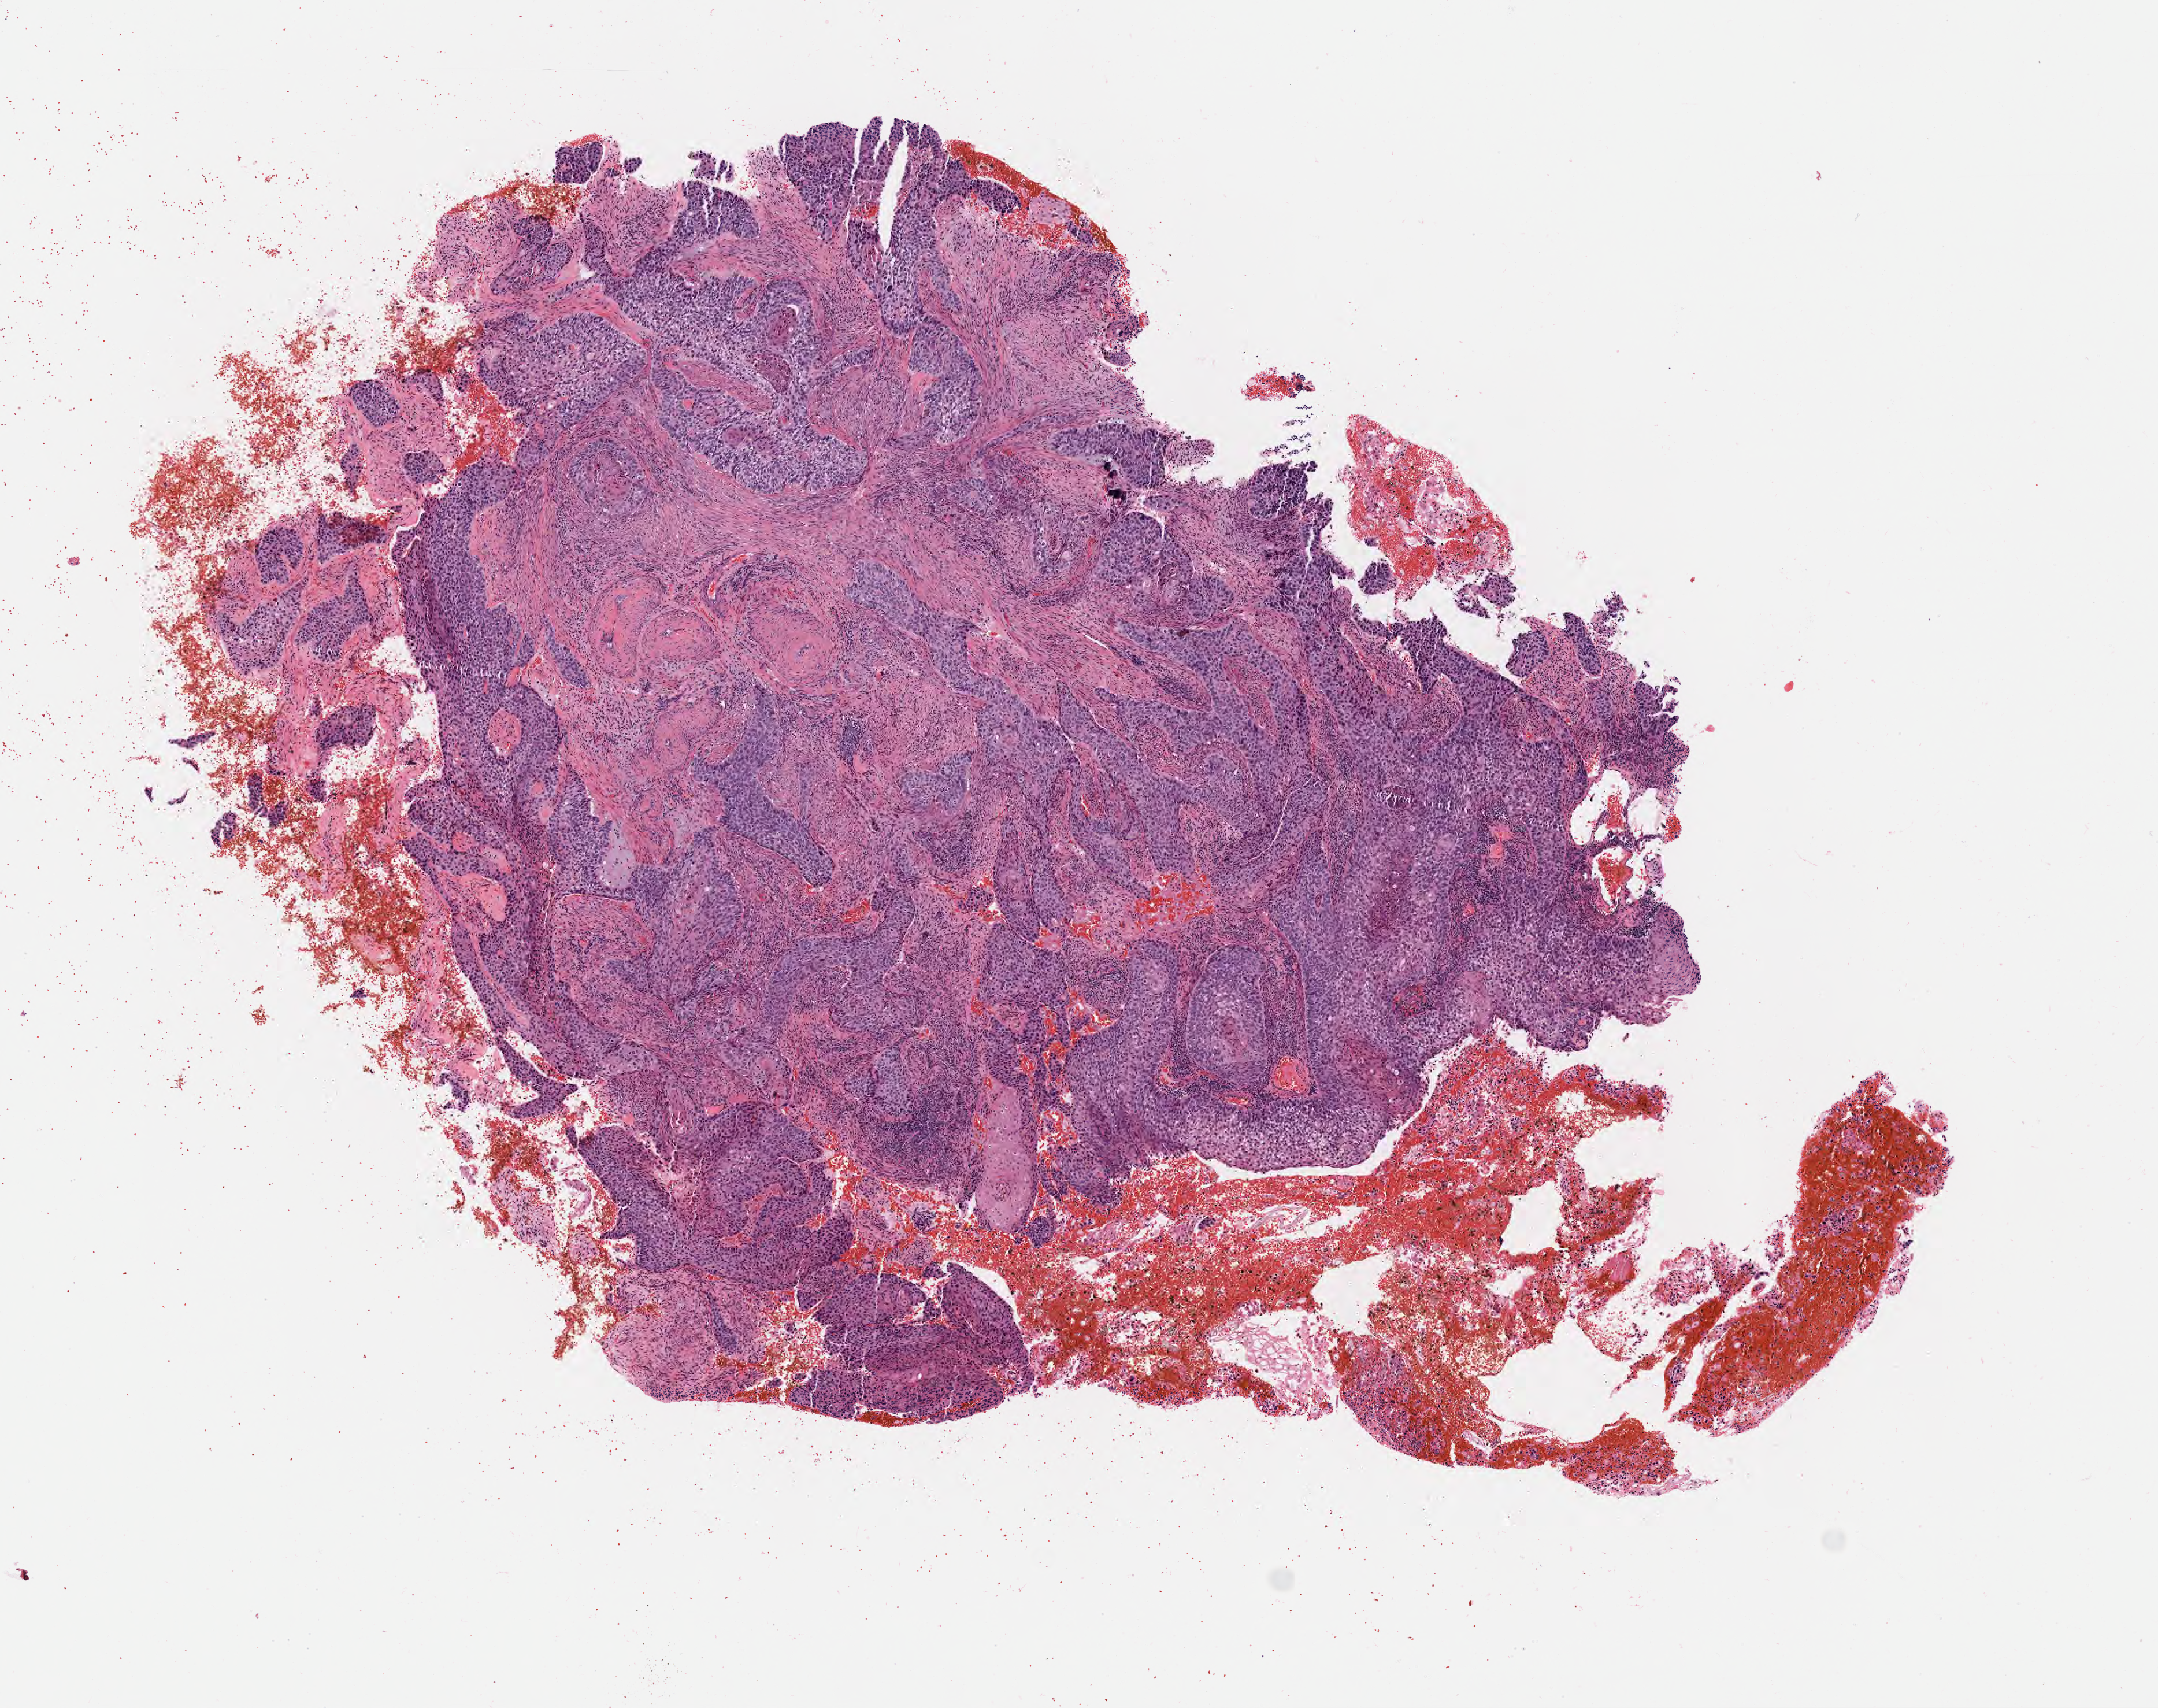
Whole-slide image, H&E stain, whole scanned area (about 7.6 x 6.0 mm) shown as a low-resolution overview. Tumor tissue. Anatomic site: cervix. Patient female; 32 years old.
• histologic diagnosis: Squamous cell carcinoma, keratinizing, NOS